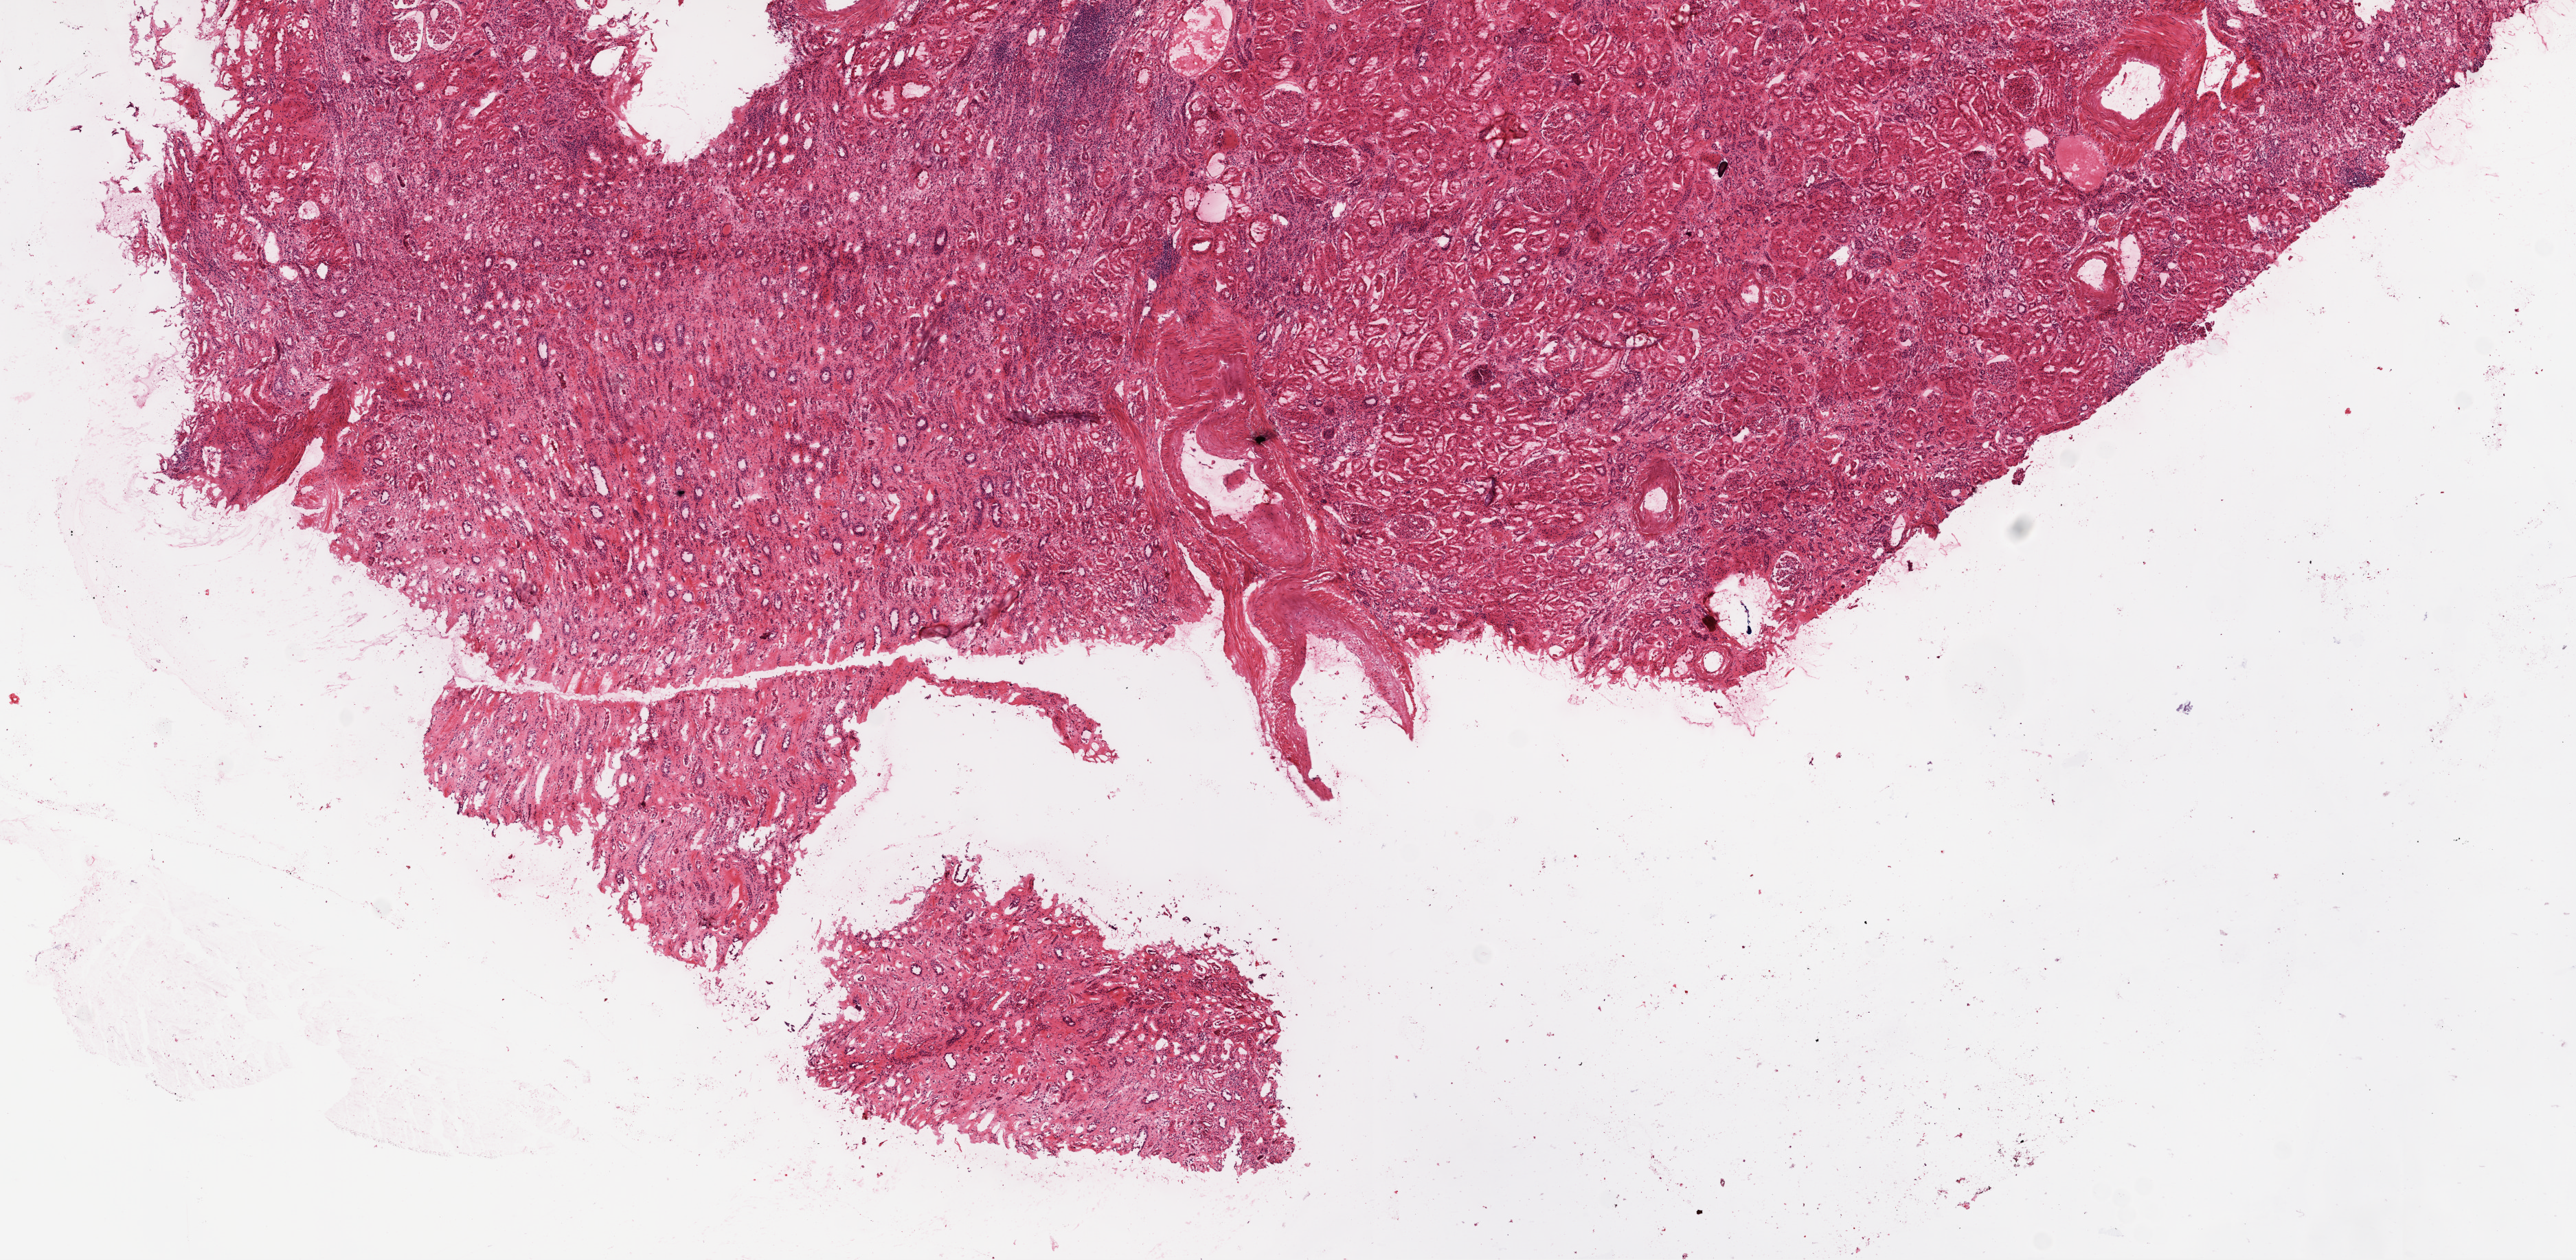
Whole-slide histology image, Hematoxylin and eosin (H&E) stained, low-resolution overview of the scanned area, about 15.0 x 7.4 mm (from a 20x scan), frozen section from the top of the tissue portion, sample: solid tissue normal (non-tumour tissue), kidney. Female patient; age at initial diagnosis 79 years.
* this section: solid tissue normal sample (biorepository sample class)
* patient diagnosis: Clear cell adenocarcinoma, NOS